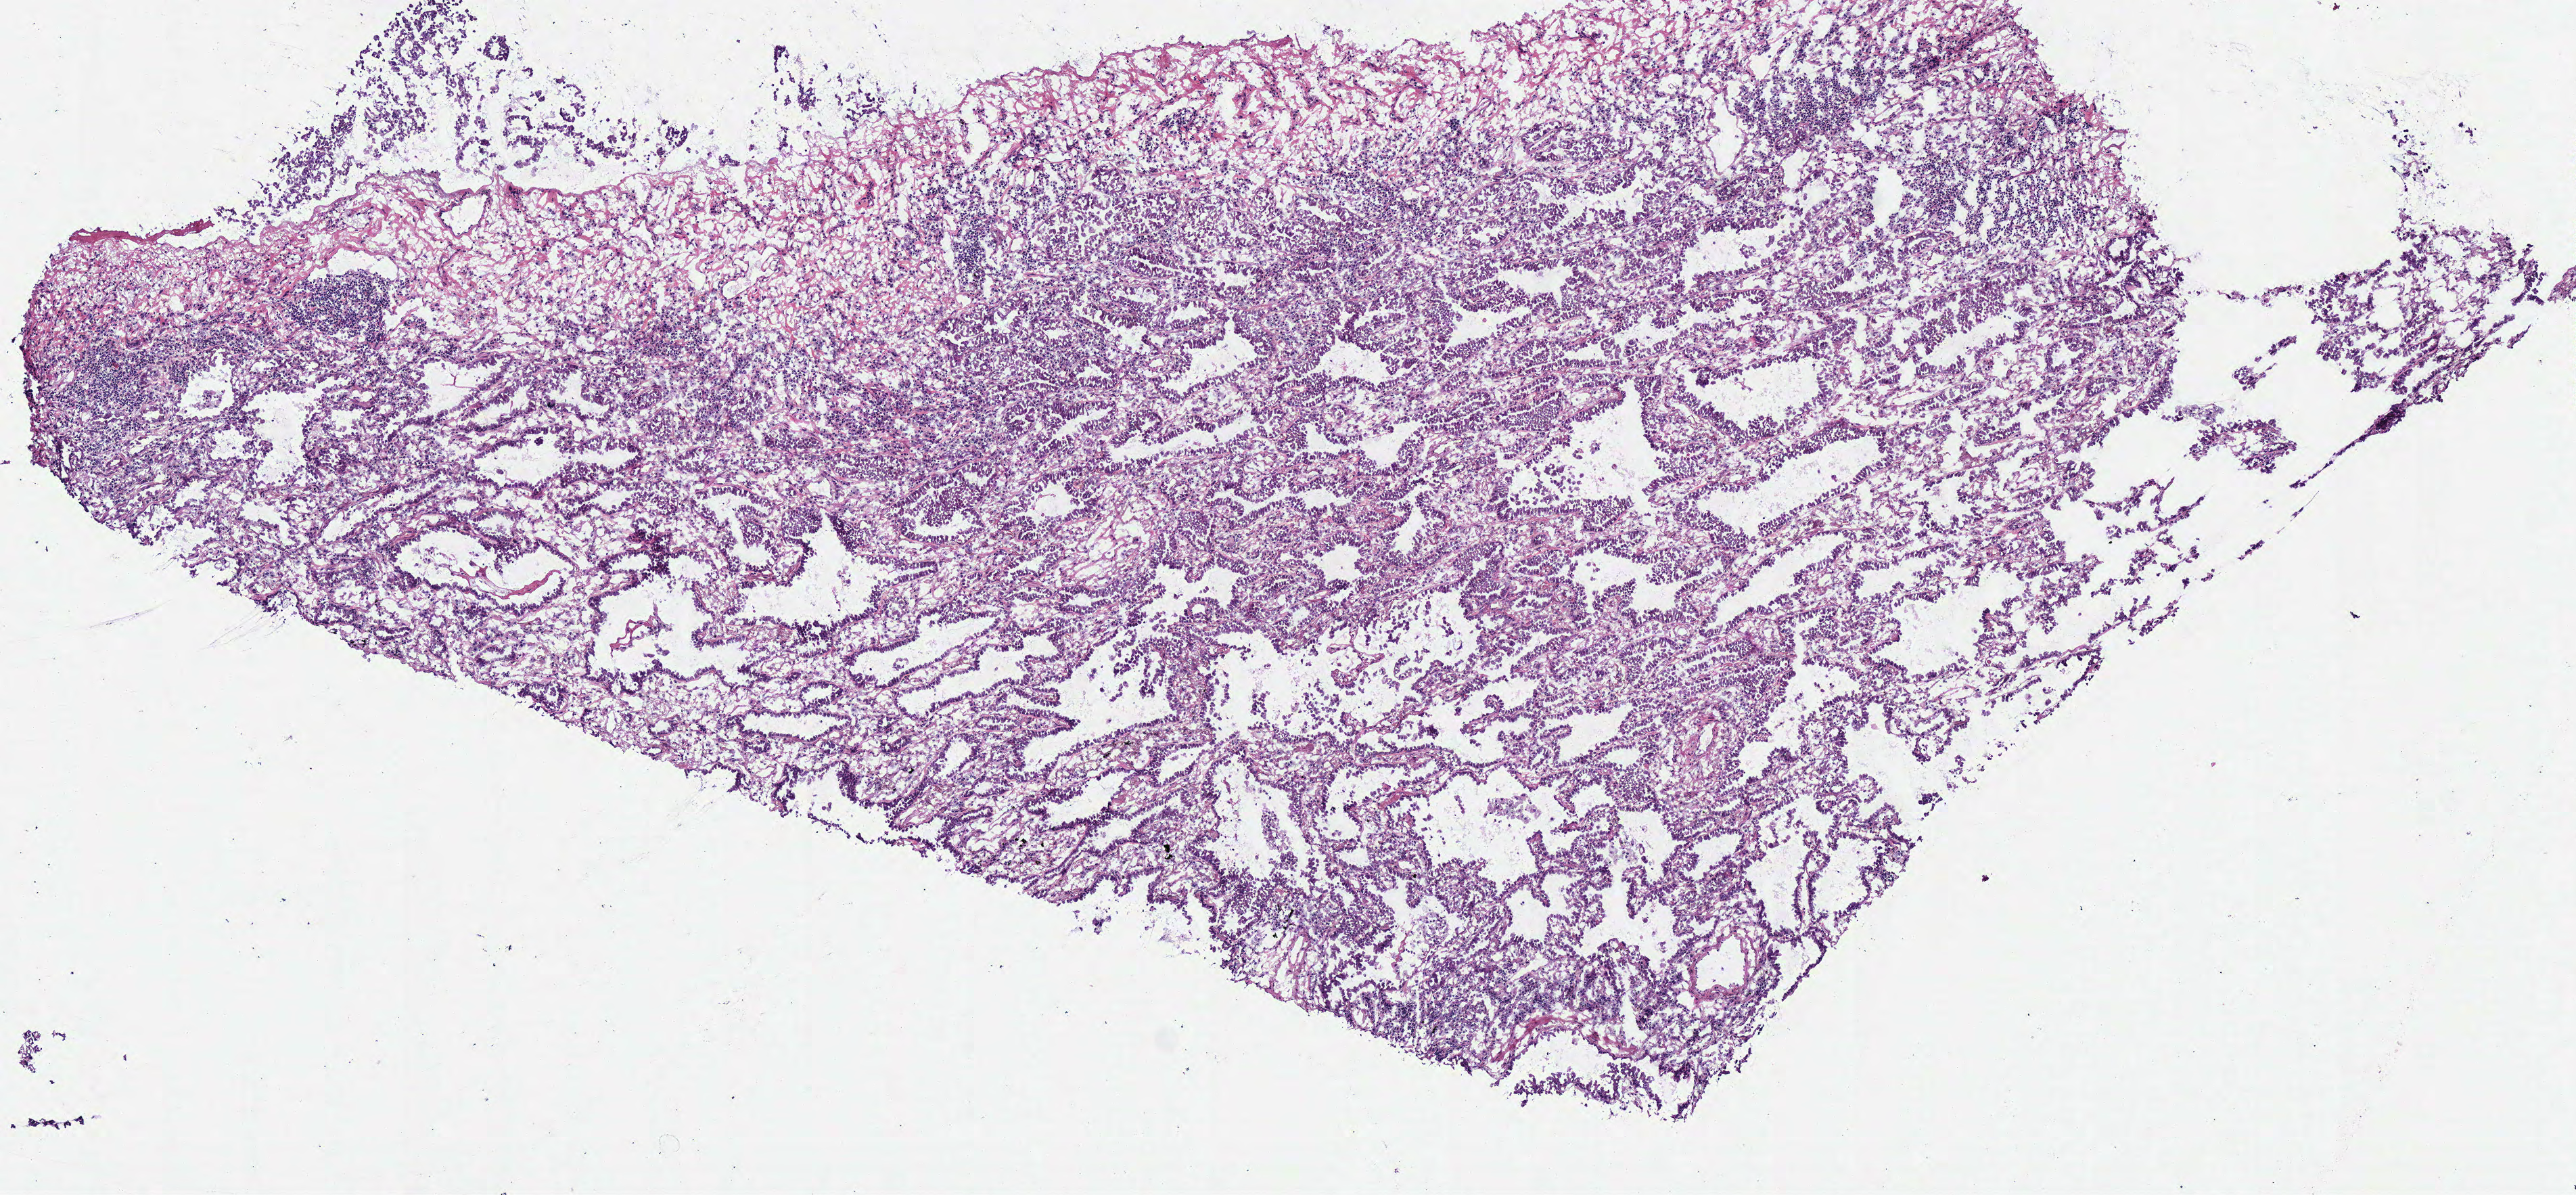
Hematoxylin and eosin (H&E) stained whole-slide image — whole scanned area (about 7.5 x 3.5 mm, acquisition: 40x scan) shown as a low-resolution overview; frozen section from the bottom of the tissue portion; primary tumour sample from the lung. Female, age 75 years at initial diagnosis. Pathologist review of this section (percent, as recorded): tumour cells 90%, tumour nuclei 80%, normal cells 0%, stromal cells 10%, necrosis 0%.
AJCC pathologic stage: IIIA (6th edition). Histologic diagnosis: Adenocarcinoma, NOS.